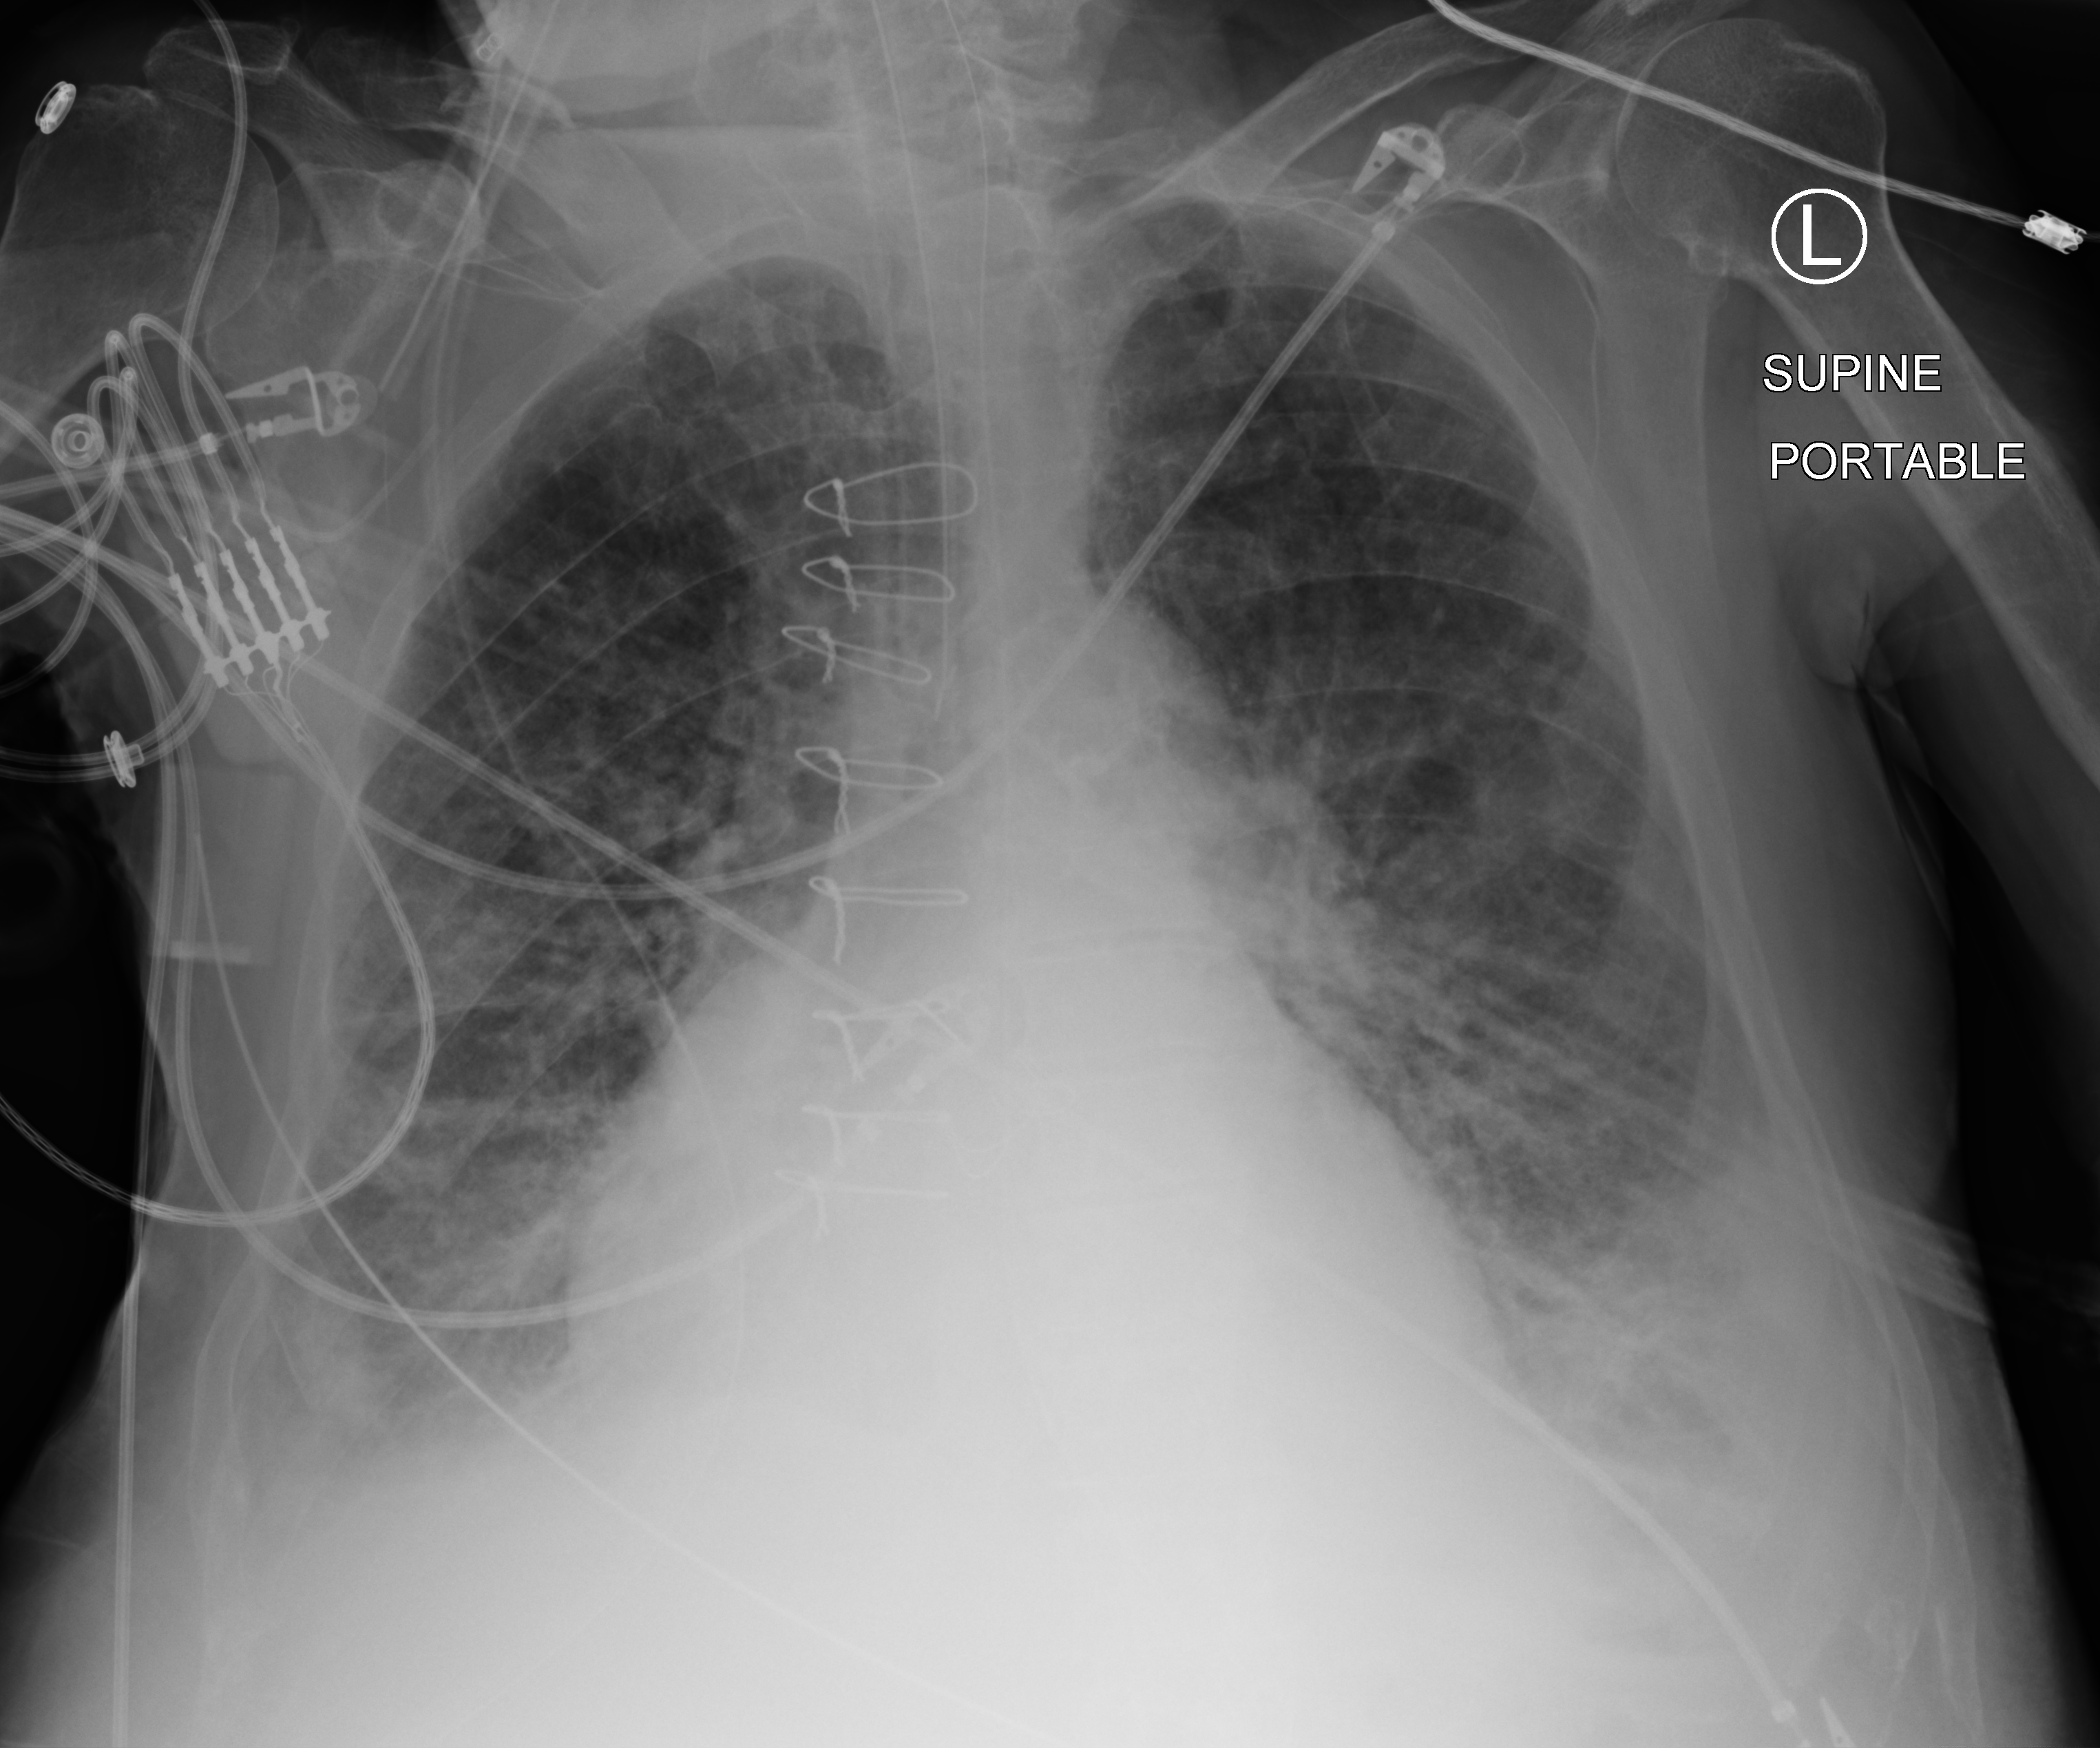
Bedside chest radiograph (computed radiography). Male patient hospitalised with COVID-19, age 75–90 years.
From the hospital-stay record, not from the radiograph (when in the stay this image was taken is not recorded): admitted to intensive care during this hospital stay: yes; mechanically ventilated during this hospital stay: yes; length of hospital stay: 40 days.